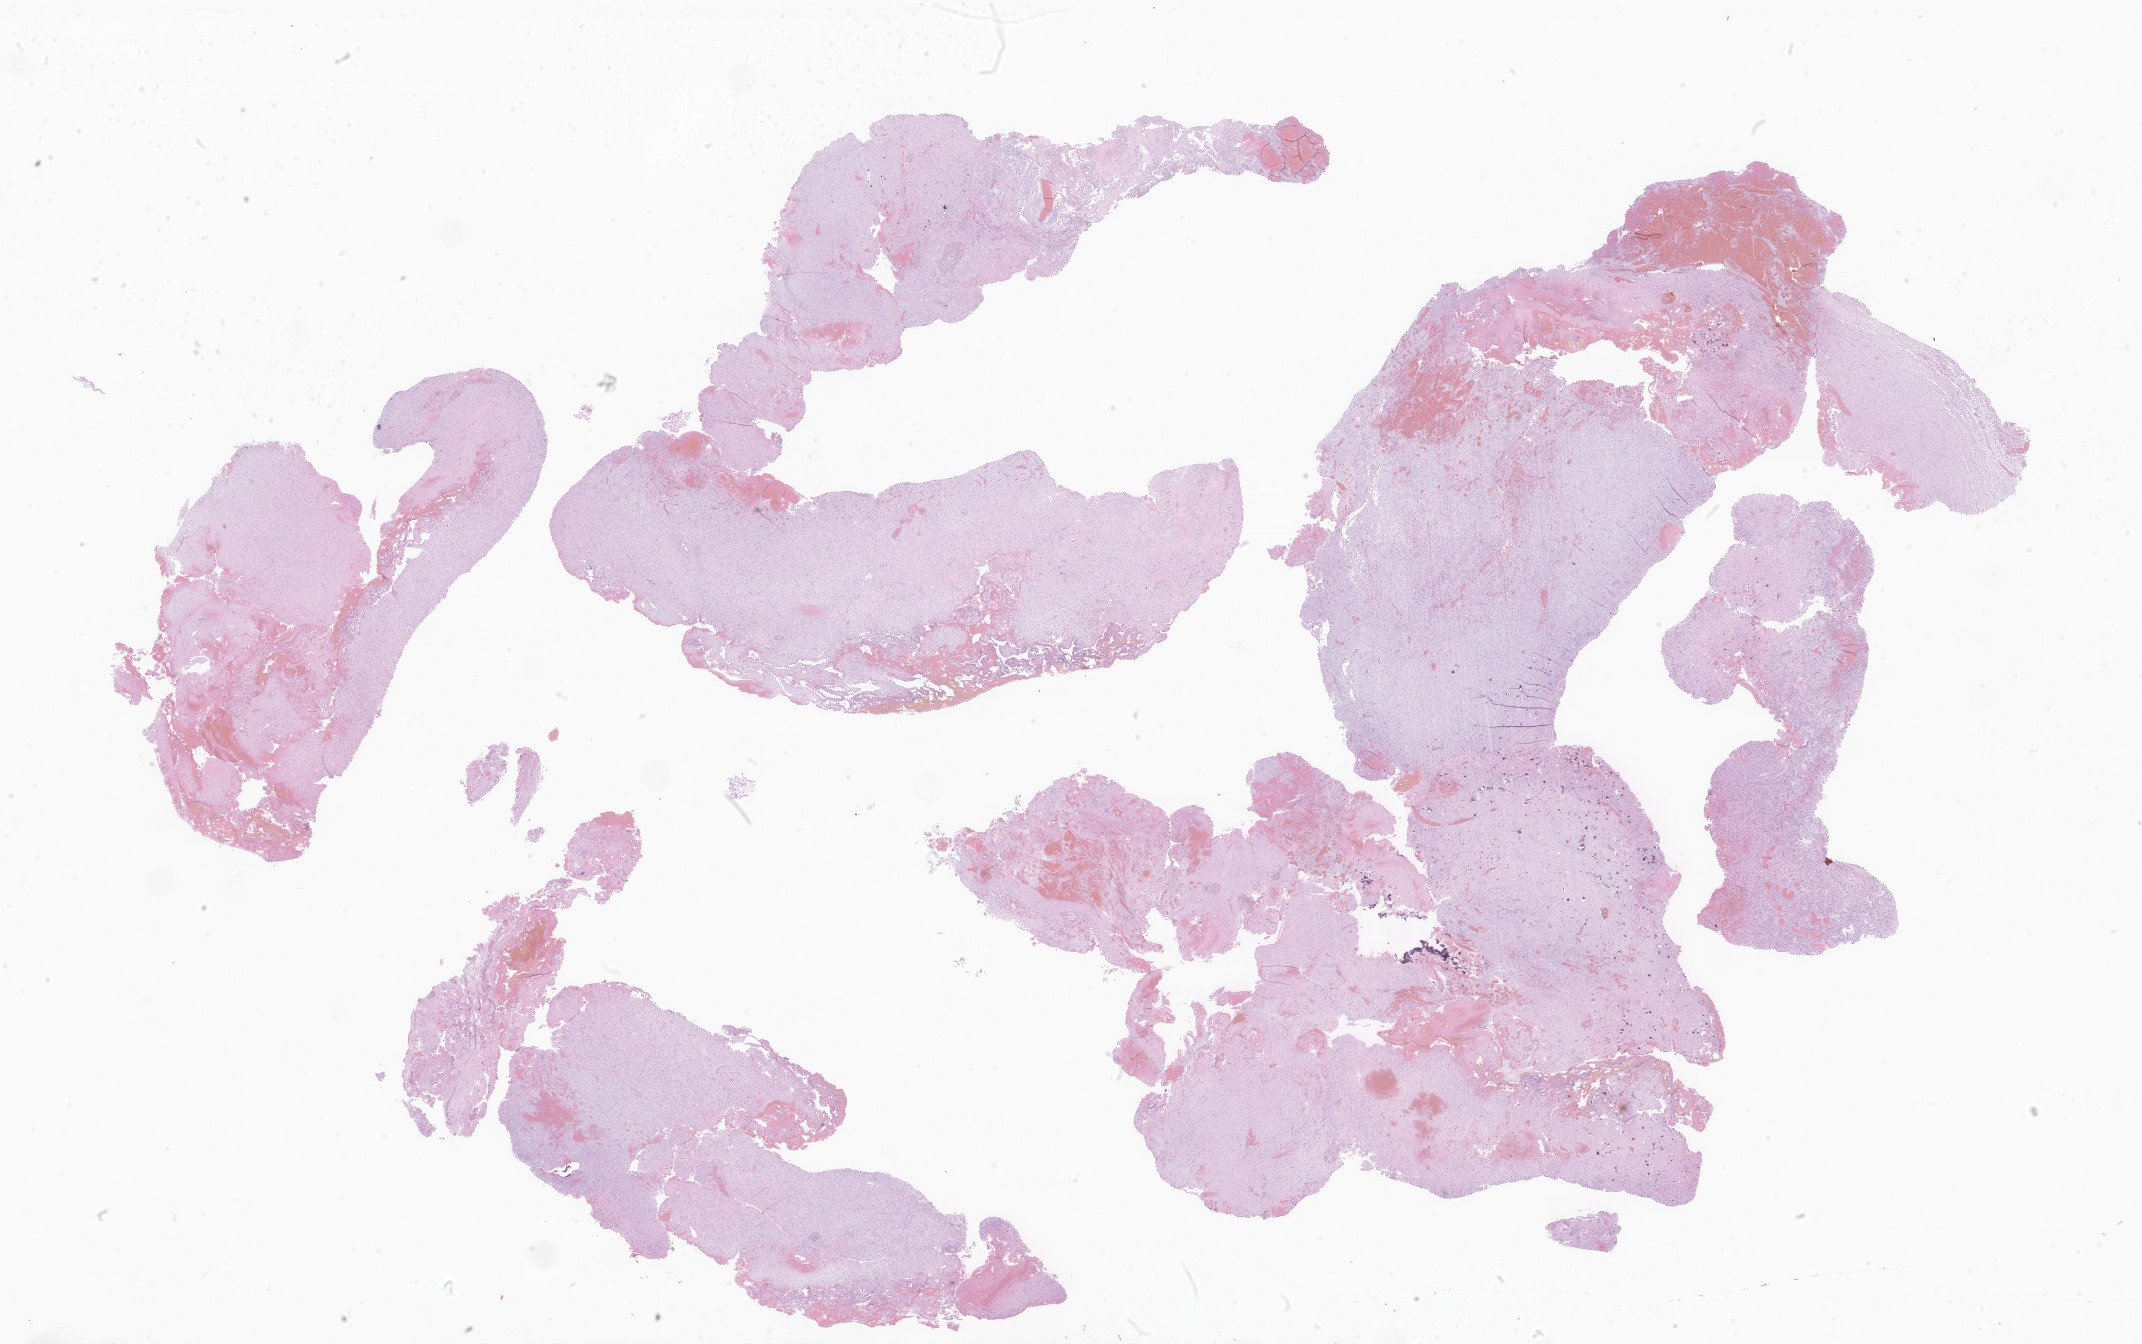
Digitized haematoxylin and eosin-stained section of tumor tissue from the brain — a low-resolution overview of the entire scanned area, about 36.1 x 22.7 mm. Formalin-fixed, paraffin-embedded (FFPE) tissue. Female patient, age 145 months (12 years 1 month).
Recorded diagnosis: Pilocytic astrocytoma.